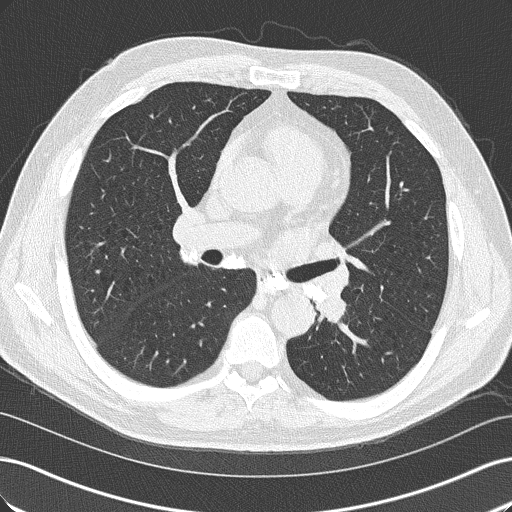
Chest CT (low-dose screening protocol), one axial image, baseline annual screen, lung window (W 1500 / L -600 HU), 2 mm slice thickness, 120 kVp, slice 77 of 152 in the series. Male participant, aged 57 years at enrolment. Former smoker at enrolment.
Expert reader's lesion annotation, bounding box <303,283,363,341> (left, top, right, bottom; pixels). No non-calcified nodule or mass ≥4 mm was recorded by the screening reader at this exam. Participant outcome: lung cancer diagnosed 363 days after this screen (after the second annual screen) — squamous cell carcinoma, NOS, left lower lobe, moderately differentiated (G2), stage IIIB (AJCC 6th edition), 38 mm at pathology.